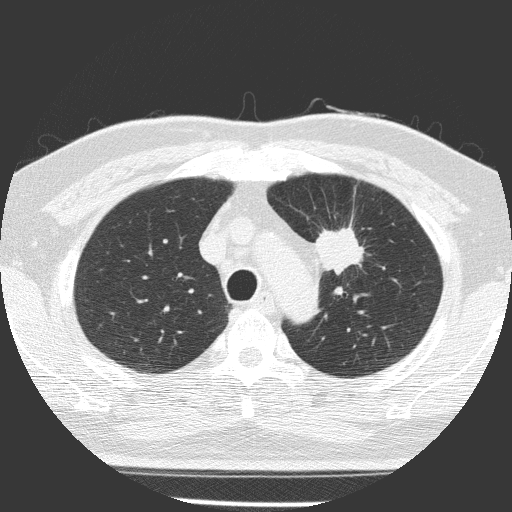
Low-dose screening chest CT, one axial slice; slice 117 of 156 in the series (ordered by position); reconstruction kernel FC51; lung window (W 1500 / L -600 HU); 2 mm slice thickness; 512 × 512 image matrix, field of view 309 × 309 mm.
Outlined on this slice (outlined manually by an expert reader):
- lesion 1 (tumor, upper lobe of left lung): bounding box (x1, y1, x2, y2) in pixels: (315, 227, 364, 274)